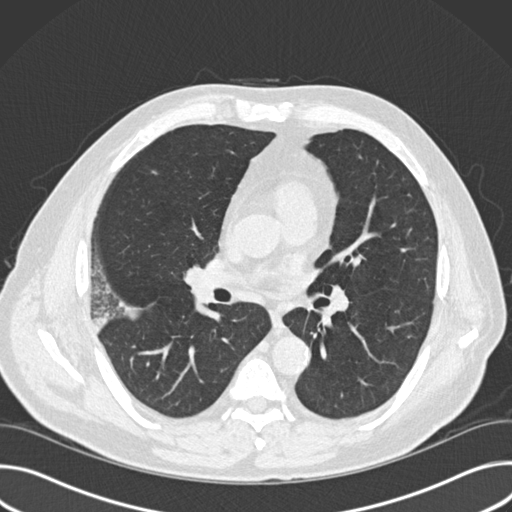
Low-dose screening chest CT, one axial slice; position 89 of 157 along the scan axis; reconstruction kernel B30f; lung window (W 1500 / L -600 HU); 512 × 512 image matrix.
Annotated regions visible in this slice (expert manual segmentation):
- lesion 1 (tumor, upper lobe of right lung): bounding box (x1, y1, x2, y2) in pixels: (117, 296, 139, 320)